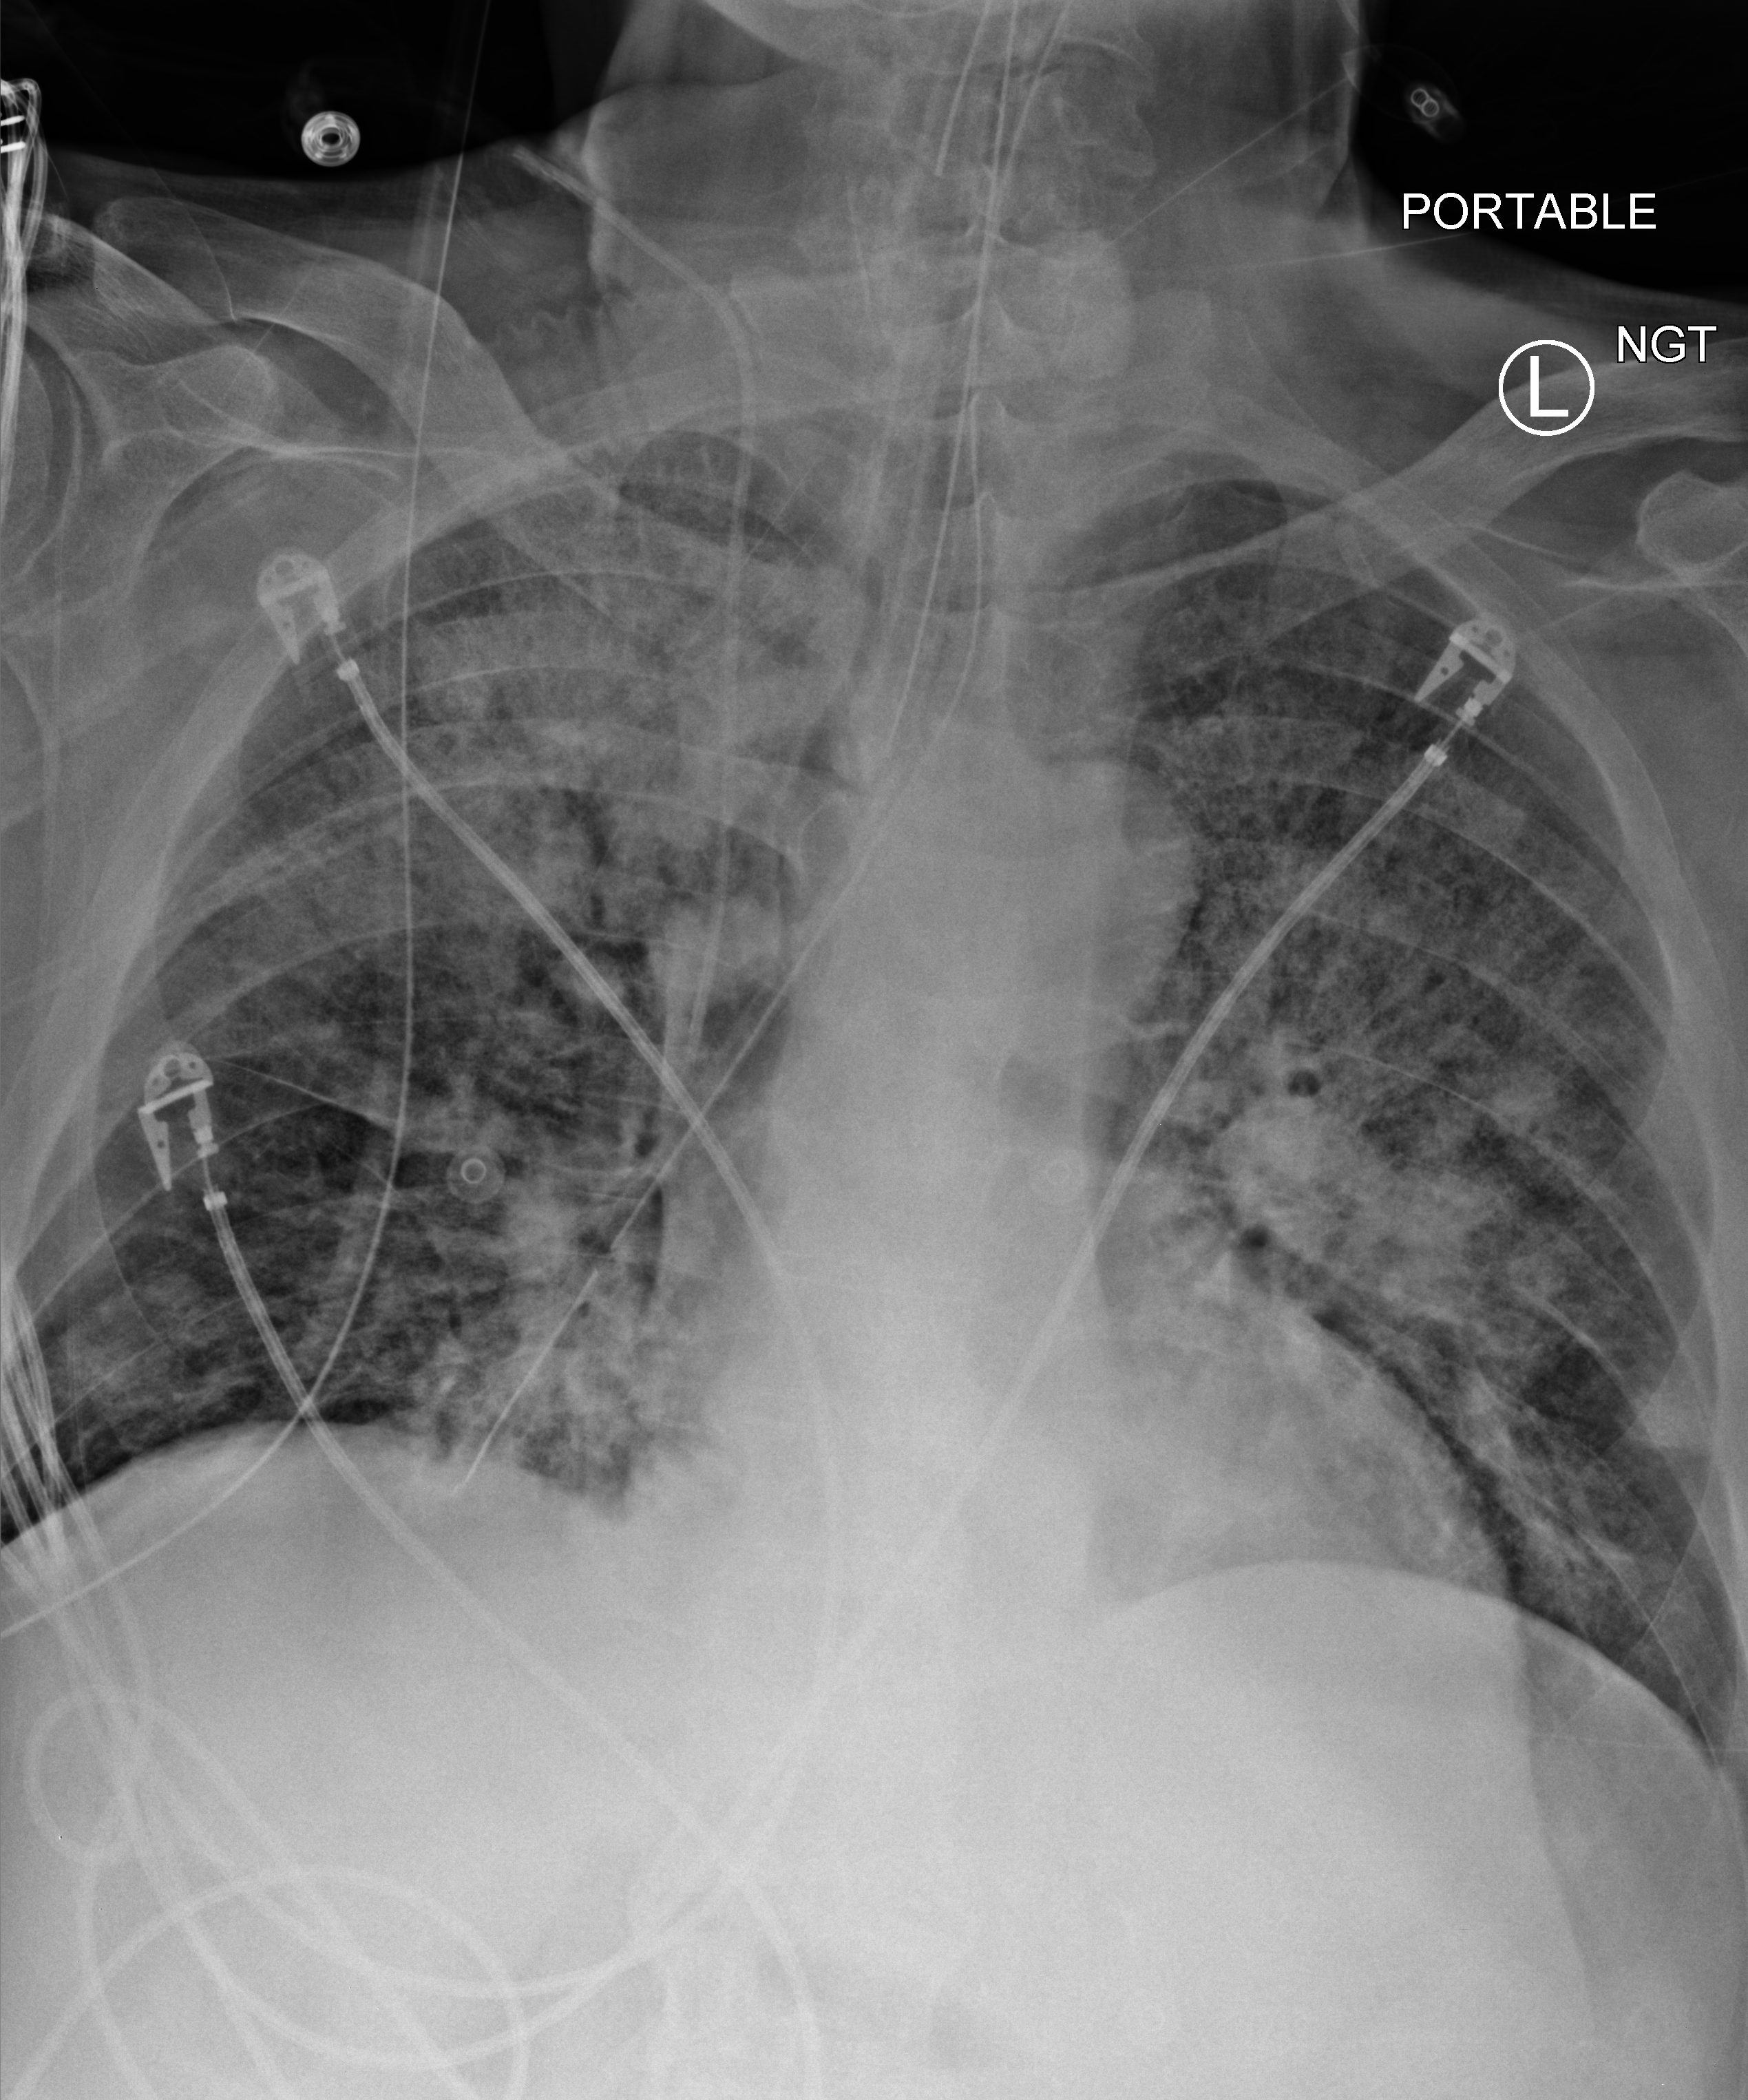
Bedside chest radiograph (computed radiography), anteroposterior (AP) projection. Male patient hospitalised with COVID-19, age 75–90 years.
From the hospital-stay record, not from the radiograph (when in the stay this image was taken is not recorded): hypertension (admission record): no; mechanically ventilated during this hospital stay: yes.